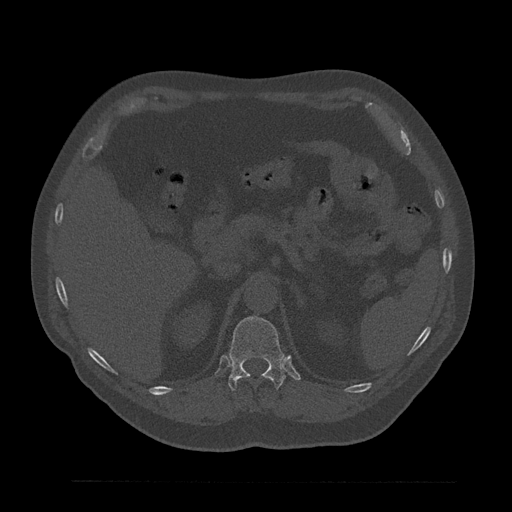
CT including the spine, one axial slice. Position 244 of 797 along the scan axis. Reconstruction kernel Br40s/3. Bone window (W 1800 / L 400 HU). 0.5 mm slice thickness. 512 × 512 image matrix, field of view 430 × 430 mm. Patient: male, 61 years. Case-level facts recorded for this patient, not image findings: primary cancer: prostate.
Structures marked on this image (semi-automatically segmented with operator editing):
- T12 vertebra: bounding box <228,316,286,391> (left, top, right, bottom; pixels)